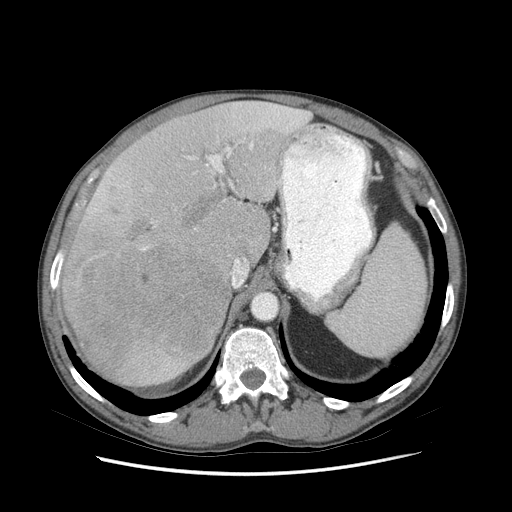
Contrast-enhanced abdominal CT (liver protocol), one axial slice; position 55 of 89 along the scan axis; reconstruction kernel STANDARD; soft-tissue window (W 400 / L 40 HU); 2.5 mm slice thickness; 512 × 512 image matrix, field of view 380 × 380 mm. Case-level facts recorded for this patient, not image findings: diagnosis: hepatocellular carcinoma (patient treated with transarterial chemoembolisation; whether this scan precedes or follows treatment is not stated here); TNM stage (as recorded): Stage-IIIB; Child-Pugh class: A; tumour differentiation: moderately differentiated; tumour nodularity: multinodular.
Annotated regions visible in this slice (semi-automatically segmented with operator editing):
- liver parenchyma outside the tumour (the mass and vessels are separate outlines, so this box may not span the whole liver): bounding box <60,100,308,386> (left, top, right, bottom; pixels)
- mass: <63,218,231,385>
- liver vessels: <89,104,303,264>